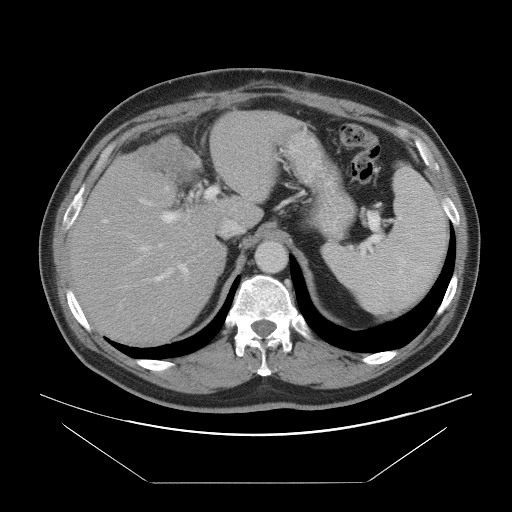
Contrast-enhanced abdominal CT, one axial slice; position 63 of 97 along the scan axis; intravenous contrast given; soft-tissue window (W 400 / L 40 HU); 5 mm slice thickness; 512 × 512 image matrix. Male patient, age 62 years. Case-level facts recorded for this patient, not image findings: diagnosis: colorectal cancer liver metastases, imaged before liver resection; multiple liver metastases: no; largest metastasis: 7 cm.
Outlined on this slice (manually delineated by an expert):
- hepatic veins: box from (x=118, y=186) to (x=244, y=267) px
- liver: (x=72, y=112)–(x=292, y=344)
- planned liver remnant (the part of the liver to remain after resection): (x=71, y=173)–(x=232, y=344)
- portal vein (with intrahepatic branches): (x=103, y=187)–(x=218, y=282)
- liver metastasis: (x=138, y=144)–(x=177, y=170)